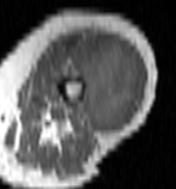
MRI of an extremity soft-tissue mass, one axial slice. Position 44 of 100 along the scan axis. MR volume resampled by the dataset authors to the PET/CT grid (not the native acquisition matrix). 176 × 189 image matrix, field of view 172 × 185 mm. Female patient. From the clinical record (not read from this slice): histological type: undifferentiated – high grade; grade: high; site of the primary tumour: left thigh.
Structures marked on this image (expert contour drawn on MRI and transferred to this co-registered scan by the dataset authors):
- gross tumour volume including surrounding oedema: bounding box [x1, y1, x2, y2] px = [57, 38, 141, 131]
- gross tumour volume (mass): [66, 39, 138, 131]